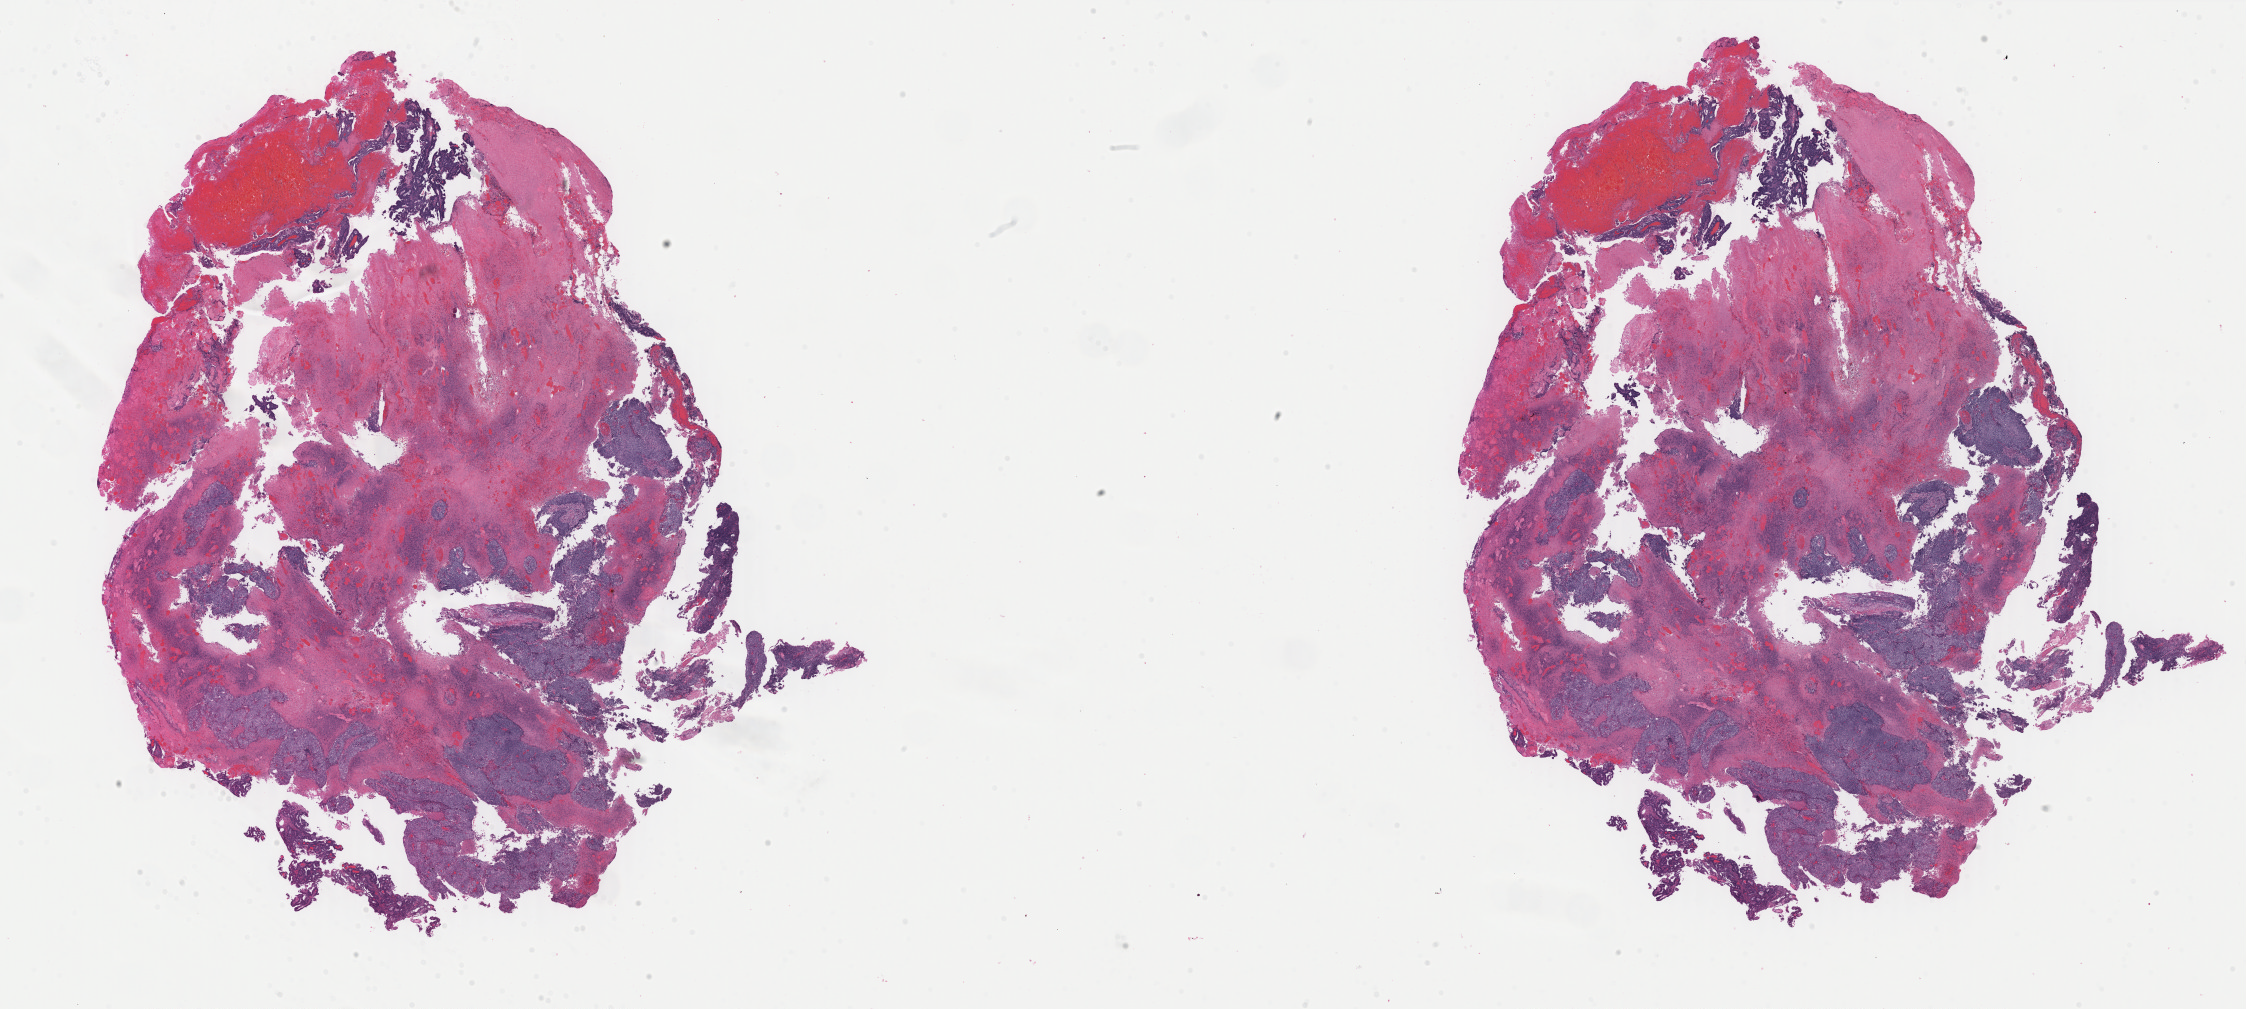
Whole-slide histology image, Hematoxylin and eosin (H&E) stained, low-resolution overview of the scanned area, about 35.5 x 16.0 mm (slide scanned at 40x); formalin-fixed paraffin-embedded (FFPE) diagnostic section; primary tumour sample from the uterus. Female patient; age at initial diagnosis 63 years. Histologic grade: G3 (poorly differentiated).
• FIGO stage: IA
• pathologic diagnosis: Endometrioid adenocarcinoma, NOS (endometrium)